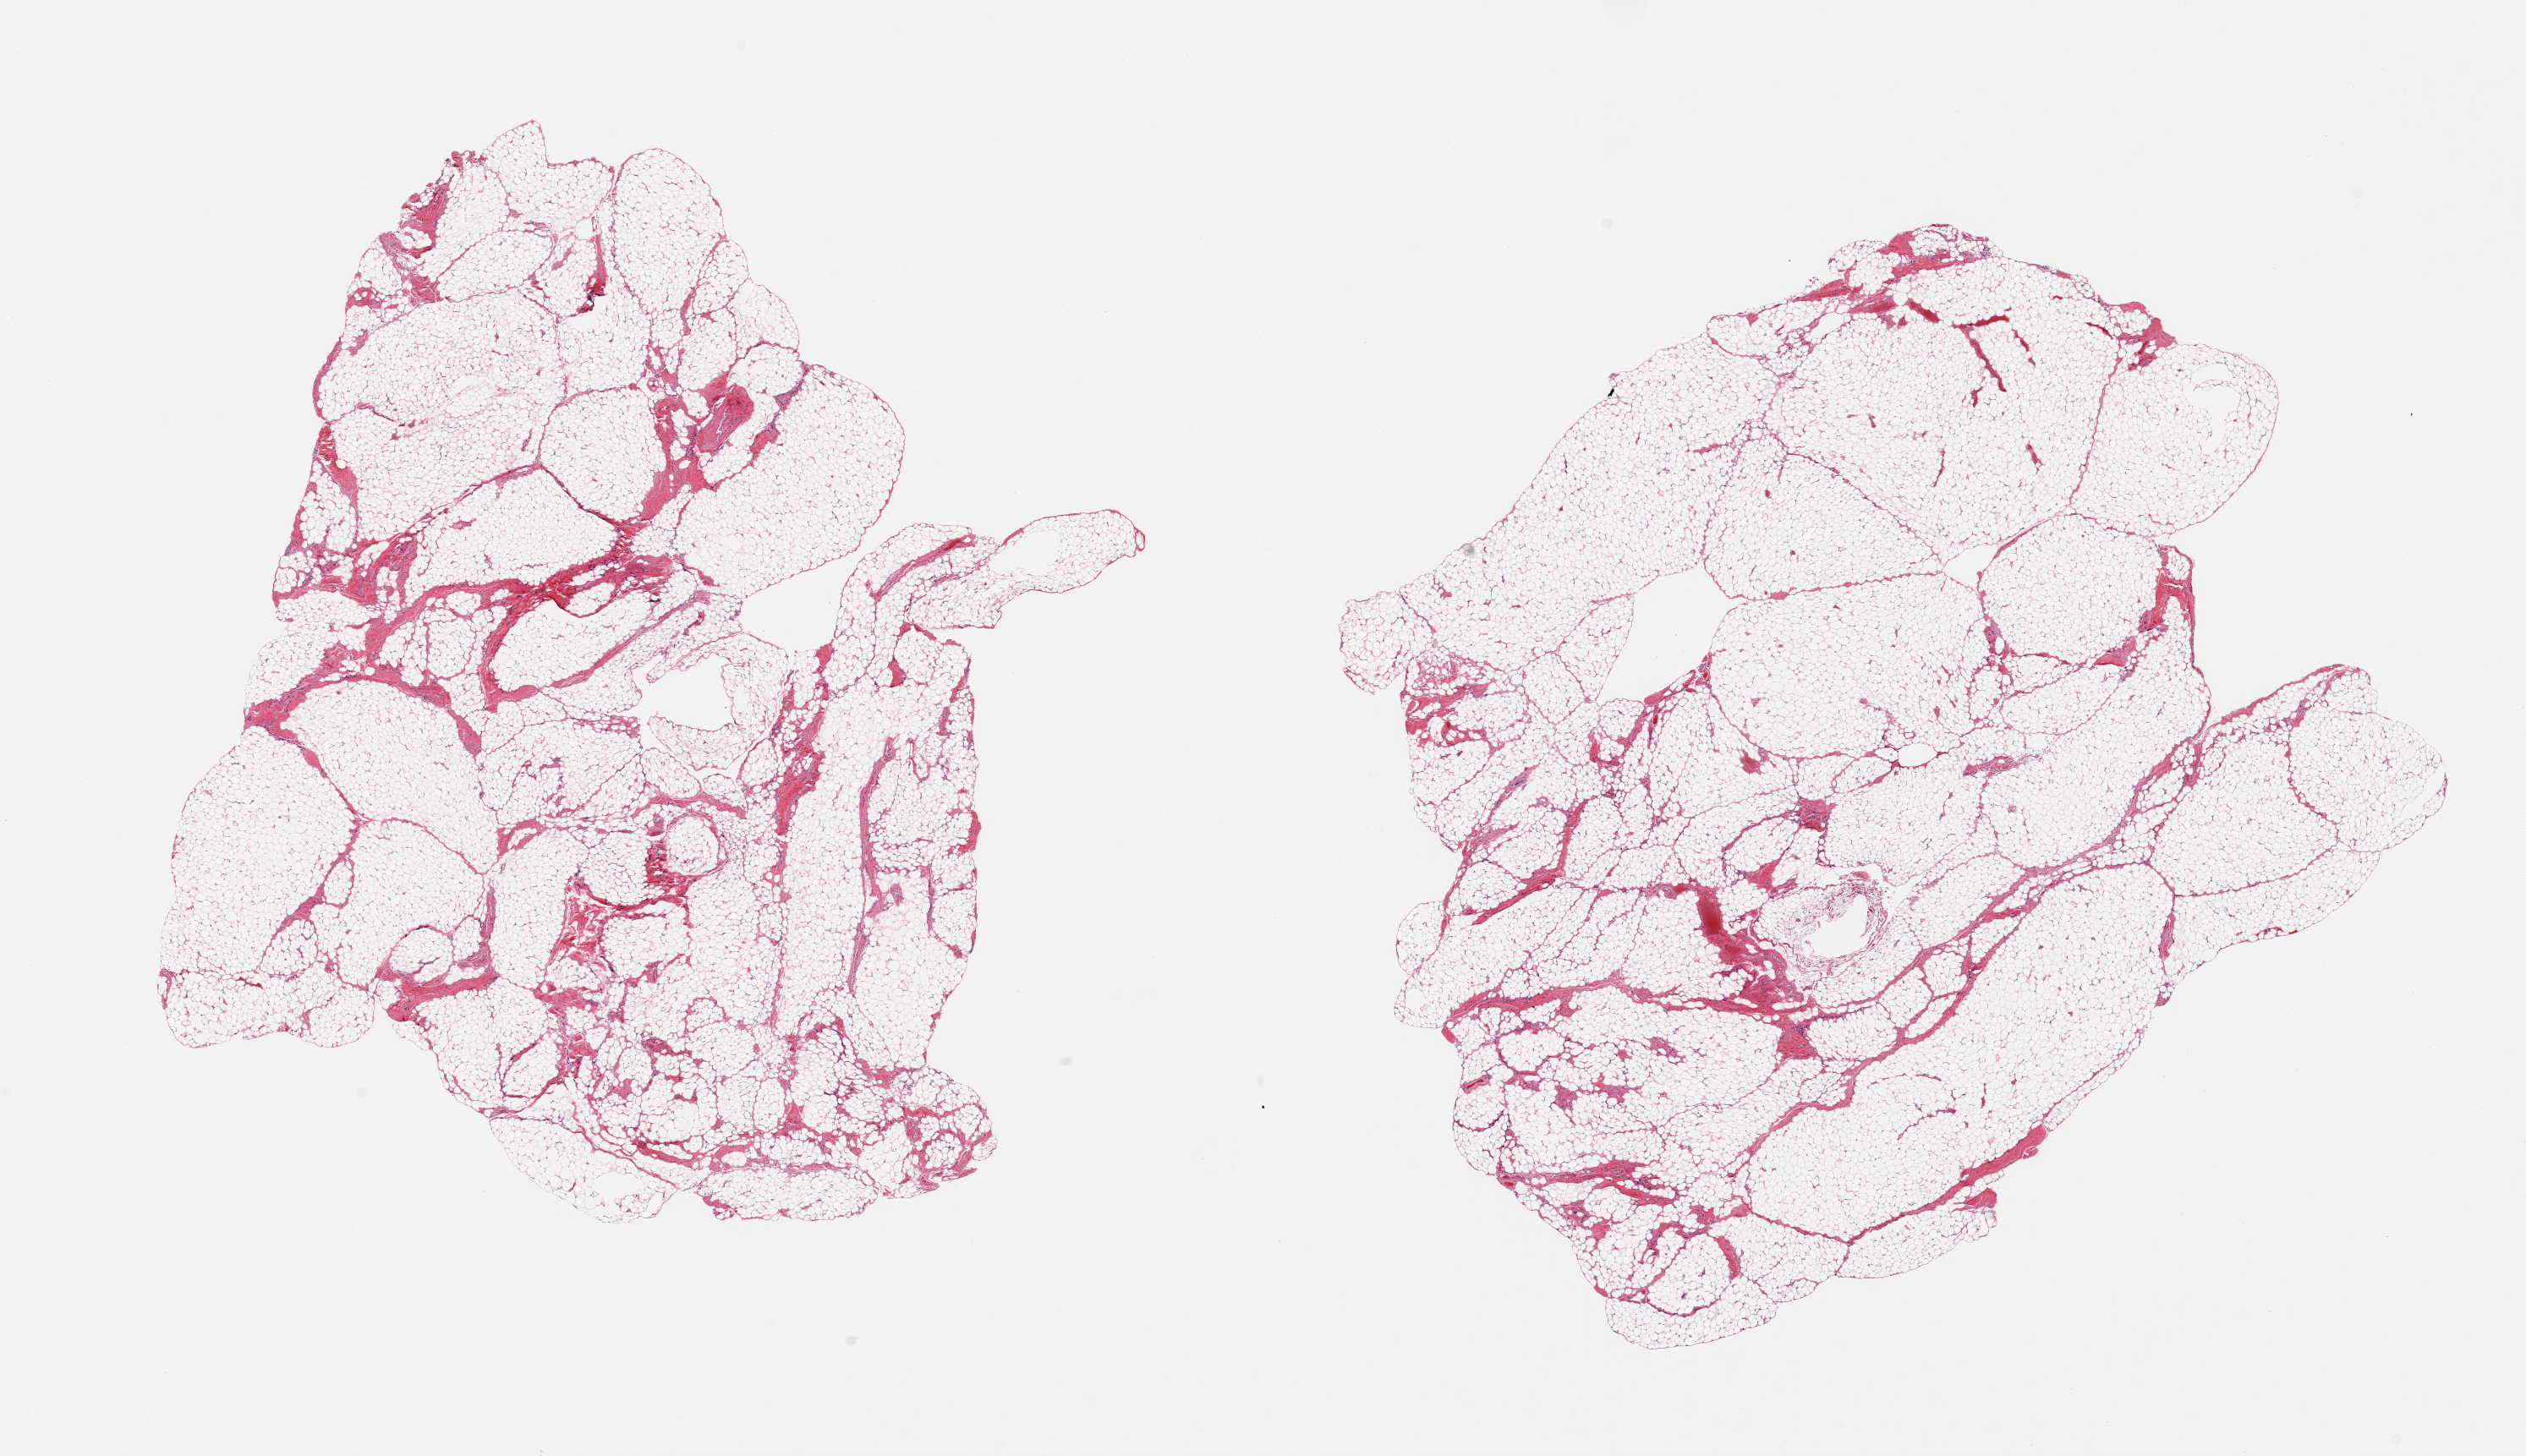
Whole-slide image, hematoxylin and eosin (H&E) stain — low-resolution overview of the scanned area, about 23.6 x 13.6 mm (slide scanned at 20x), PAXgene-fixed paraffin-embedded (PFPE) section, sampled site (target tissue): omentum, donor tissue sample. Donor sex: male.
Reviewer comment on this tissue sample: 2 pieces; lobulated adipose tissue with fibrovascular component.